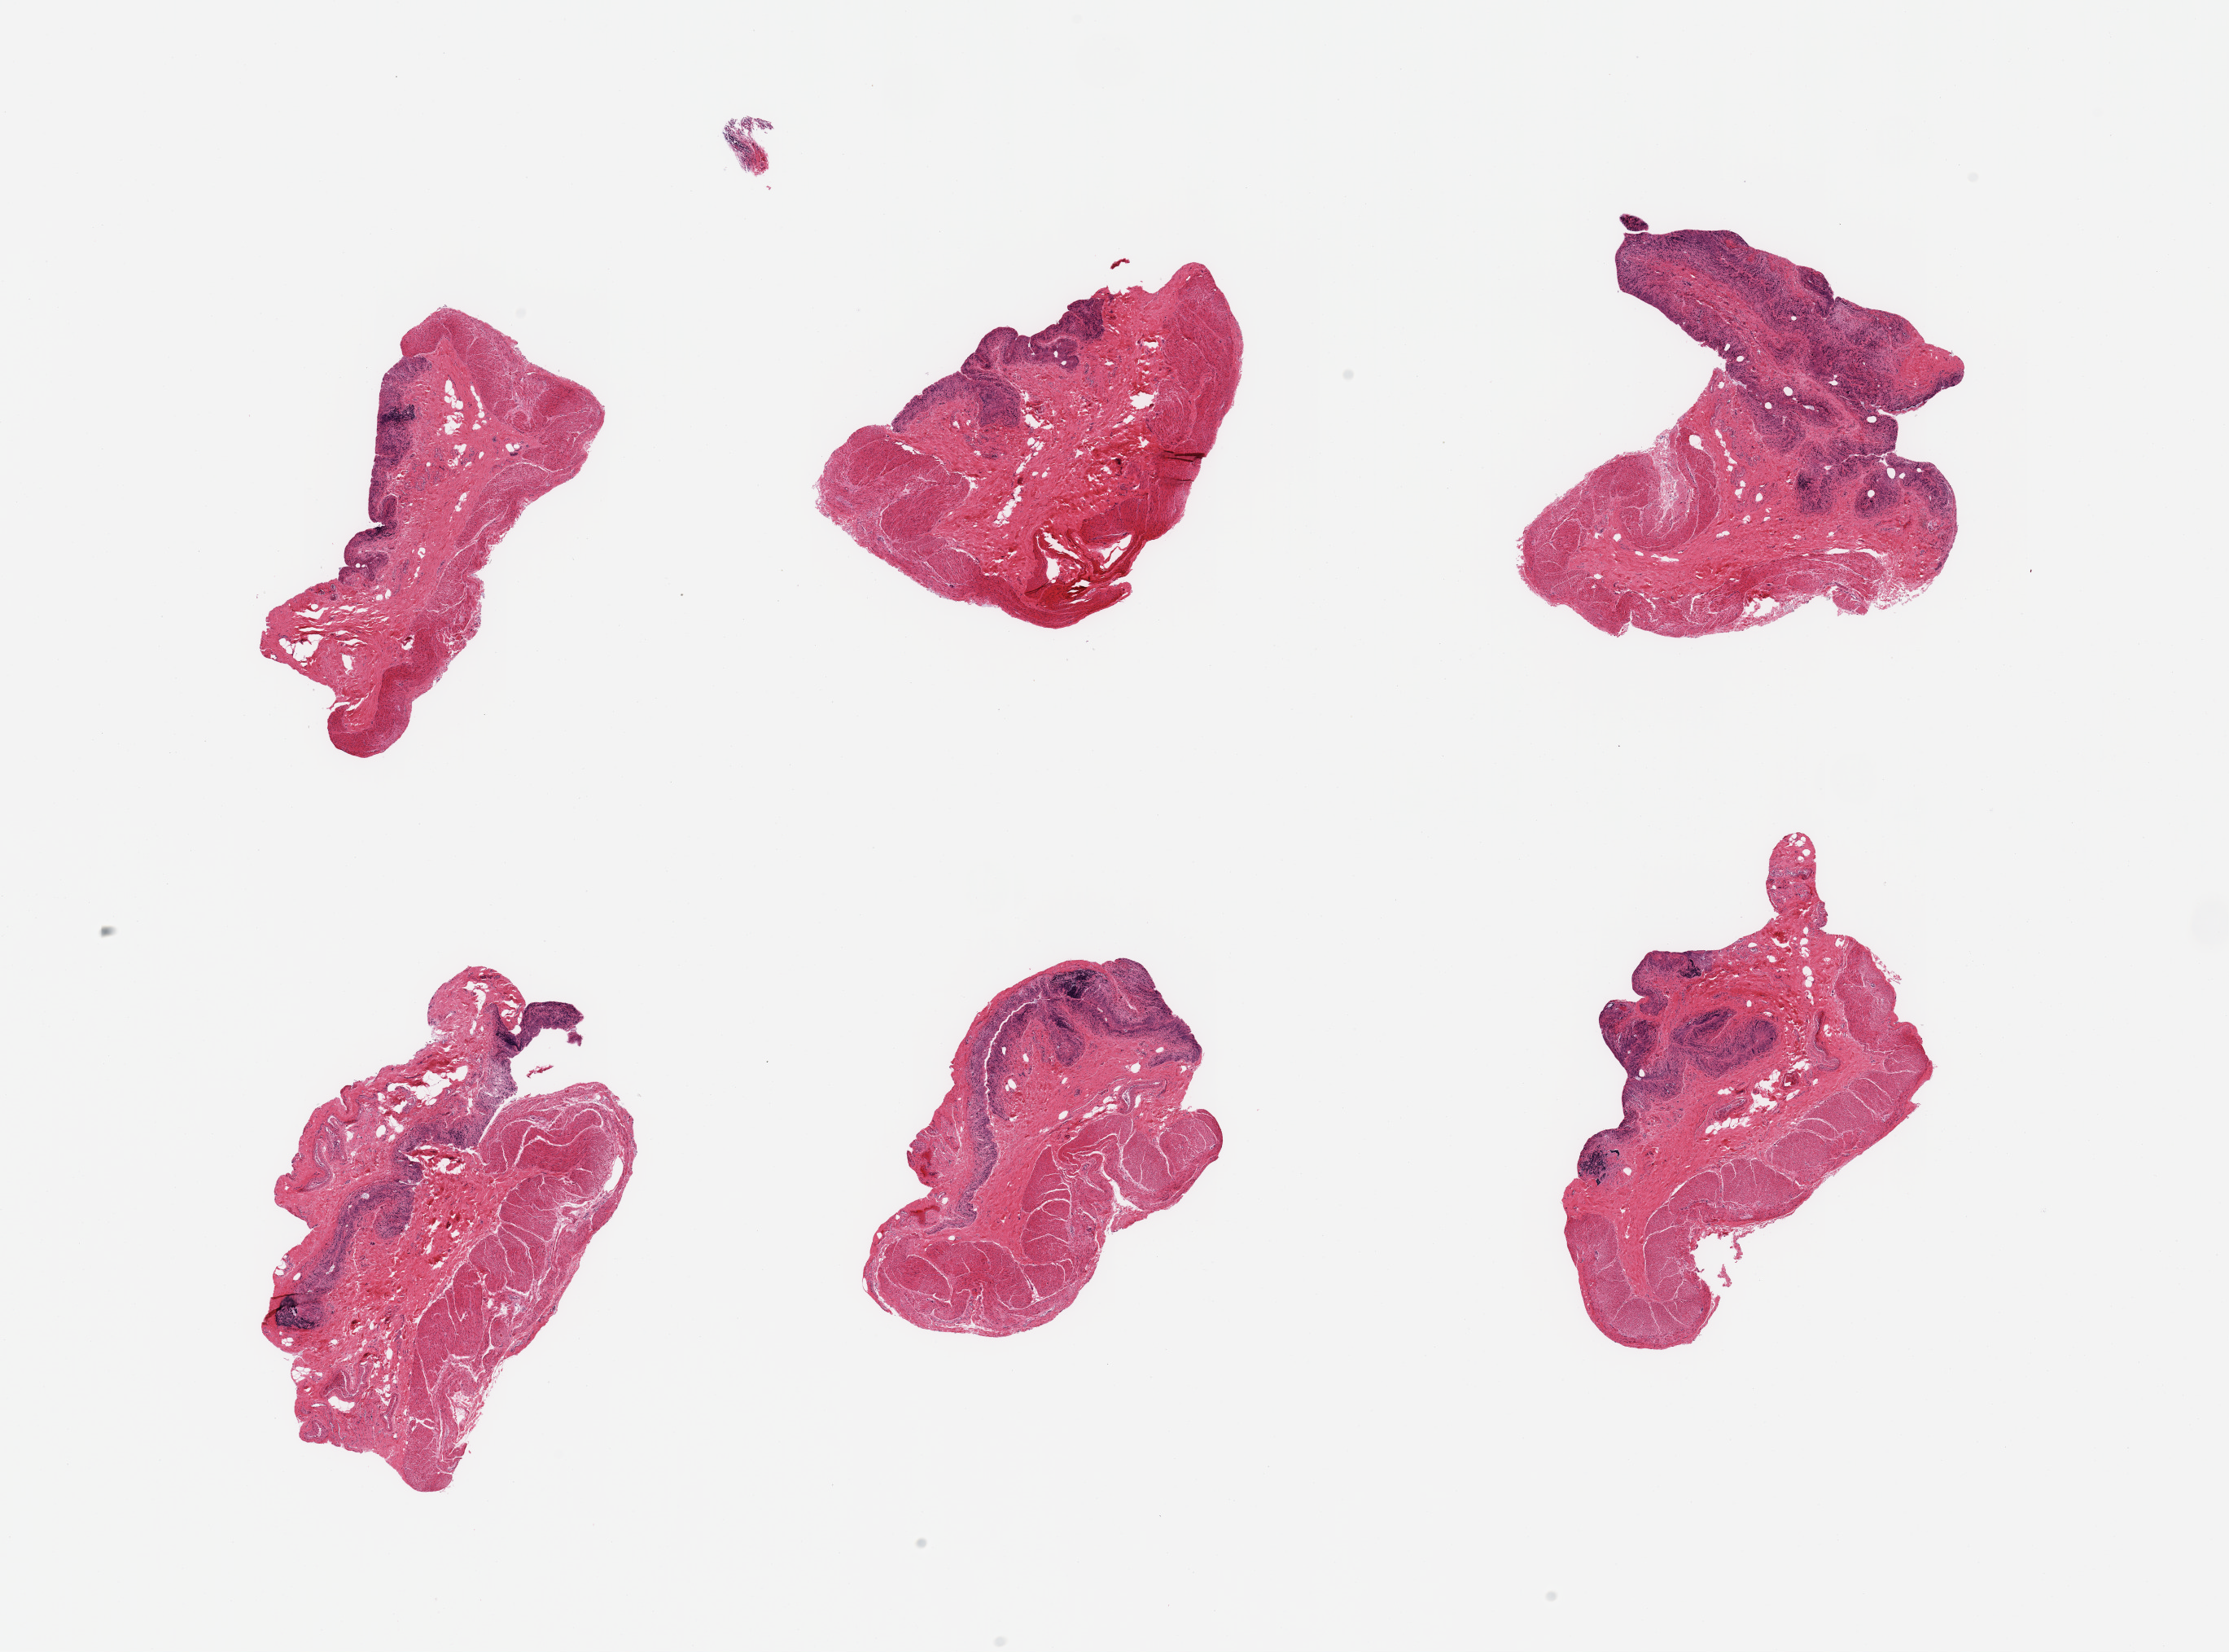
Digitized hematoxylin and eosin (H&E)-stained section, low-resolution overview of the scanned area, about 21.7 x 16.0 mm, PAXgene-fixed, paraffin-embedded tissue, section of transverse colon (target tissue), donor tissue sample. Donor sex: male.
Review note (as recorded): 6 pieces, target mucosa is ~0.25mm, lamina propria only, glandular elements with advanced autolysis.